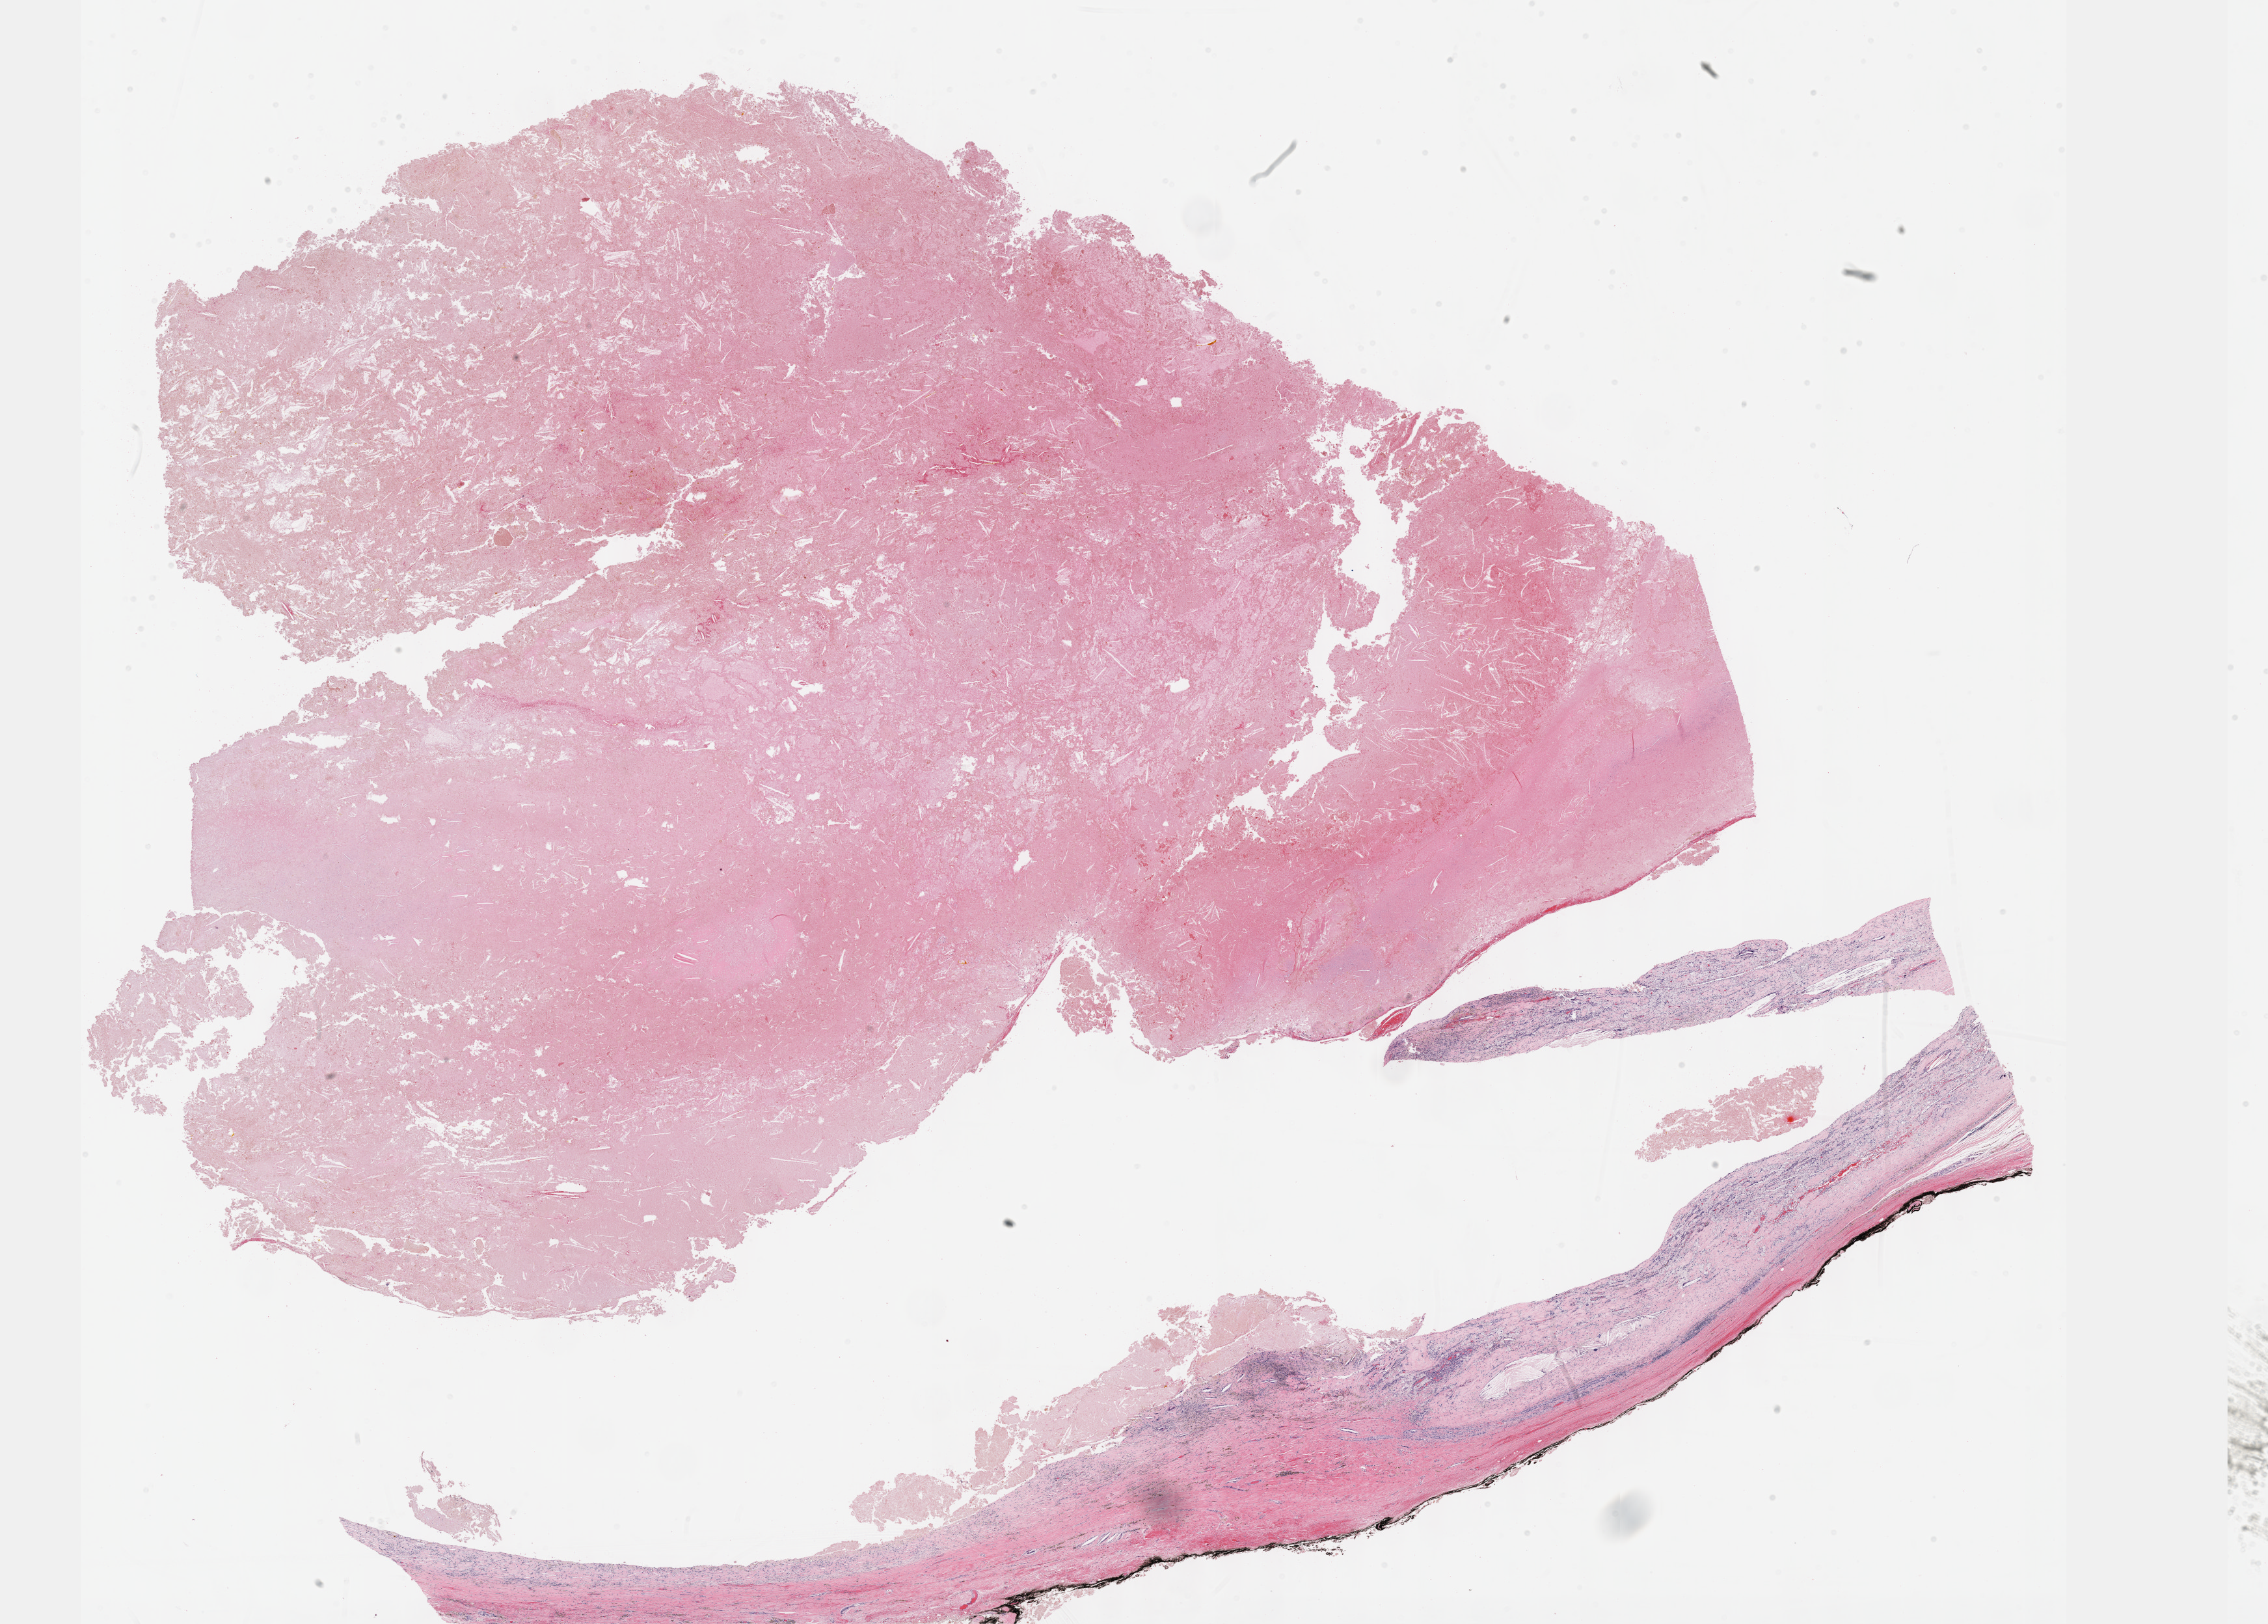
H&E-stained whole-slide image, shown as a low-resolution overview of the whole scanned area (about 28.2 x 20.2 mm), formalin-fixed paraffin-embedded (FFPE) diagnostic section, sample: primary tumour, kidney. Male patient; age at initial diagnosis 85 years.
AJCC pathologic stage: I (7th edition). Pathologic diagnosis: Papillary adenocarcinoma, NOS.